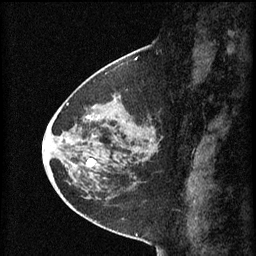
Breast MRI (dynamic contrast-enhanced), one sagittal slice; position 29 of 60 along the scan axis; 3 images stored at this slice position (order not interpretable as contrast timing); 1.5 T; TE 4.2 ms, TR 8.2 ms; 2 mm slice thickness; 256 × 256 image matrix, field of view 200 × 200 mm. Female patient, age 45 years.
Outlined on this slice (semi-automatic segmentation, software-assisted and operator-edited):
- analysis volume of interest (the breast-tissue region the enhancement analysis was run in; not a lesion): bounding box [x1, y1, x2, y2] px = [80, 102, 157, 171]
- tumour enhancement mask (voxels above the 70 % enhancement threshold inside the analysis volume of interest): [87, 158, 96, 167]